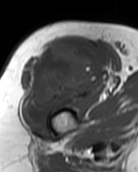
MRI of an extremity soft-tissue mass, one axial slice. Slice 73 of 99 in the series (ordered by position). MR volume resampled by the dataset authors to the PET/CT grid (not the native acquisition matrix). 3.27 mm slice thickness. 138 × 172 image matrix. Female patient. From the clinical record (not read from this slice): histological type: pleiomorphic undifferentiated sarcoma; grade: high; site of the primary tumour: right quadricep.
Annotated regions visible in this slice (expert contour drawn on MRI and transferred to this co-registered scan by the dataset authors):
- gross tumour volume including surrounding oedema: bounding box [x1, y1, x2, y2] px = [21, 43, 100, 120]
- gross tumour volume (mass): [21, 43, 100, 120]